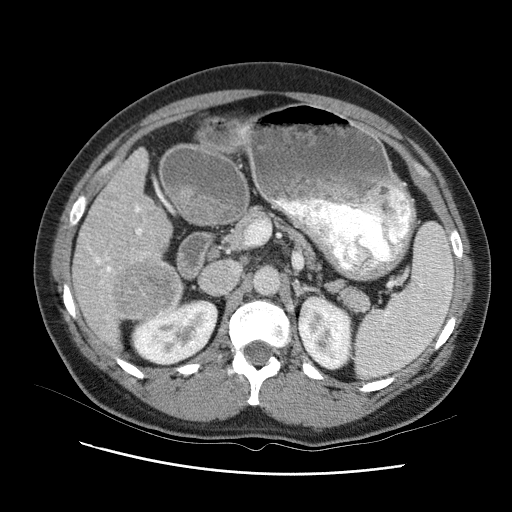
Contrast-enhanced abdominal CT (liver protocol), one axial slice. Slice 46 of 95 in the series (ordered by position). Reconstruction kernel STANDARD. 120 kVp. One of 2 acquisitions stored at this slice position. Soft-tissue window (W 400 / L 40 HU). 512 × 512 image matrix, field of view 360 × 360 mm. From the clinical record (not read from this slice): diagnosis: hepatocellular carcinoma (patient treated with transarterial chemoembolisation; whether this scan precedes or follows treatment is not stated here); TNM stage (as recorded): Stage-I; Child-Pugh class: B; tumour nodularity: uninodular.
Annotated regions visible in this slice (semi-automatic segmentation, software-assisted and operator-edited):
- liver parenchyma outside the tumour (the mass and vessels are separate outlines, so this box may not span the whole liver): bounding box [x1, y1, x2, y2] px = [69, 138, 184, 362]
- mass: [119, 248, 187, 315]
- liver vessels: [103, 163, 158, 351]